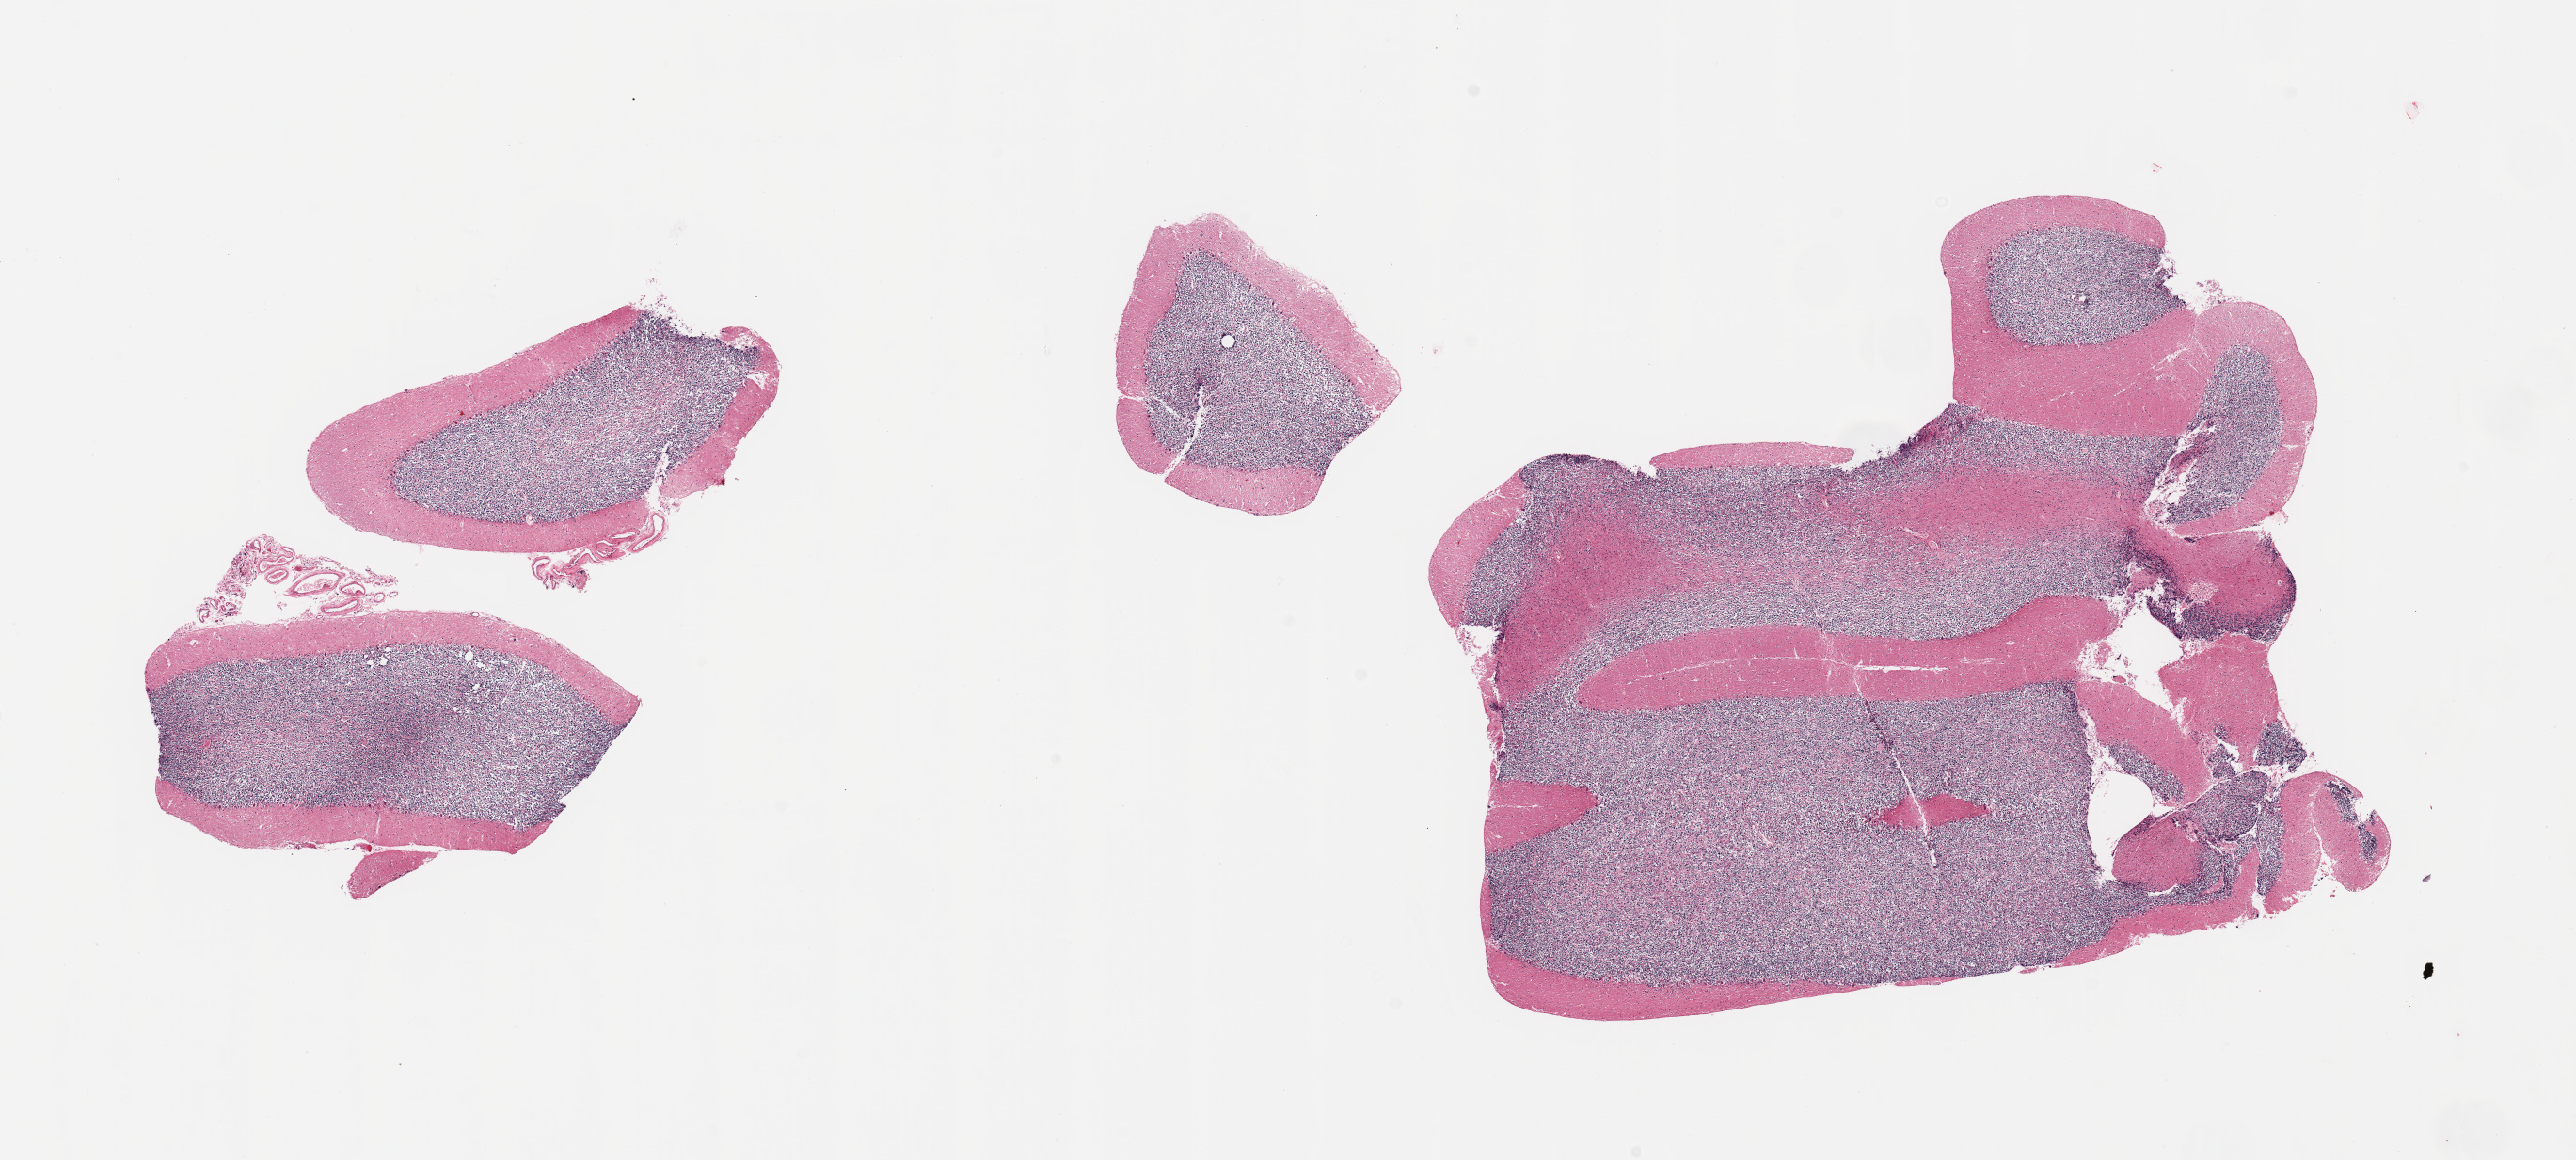
Whole-slide image, hematoxylin and eosin (H&E) stain, a low-resolution overview of the entire scanned area, about 21.7 x 9.8 mm (acquisition: 20x scan). PAXgene-fixed paraffin-embedded (PFPE) section. Target tissue: cerebellum. Donor tissue sample. Male donor.
- reviewer comment on this tissue sample: 1 large & several small fragmented pieces